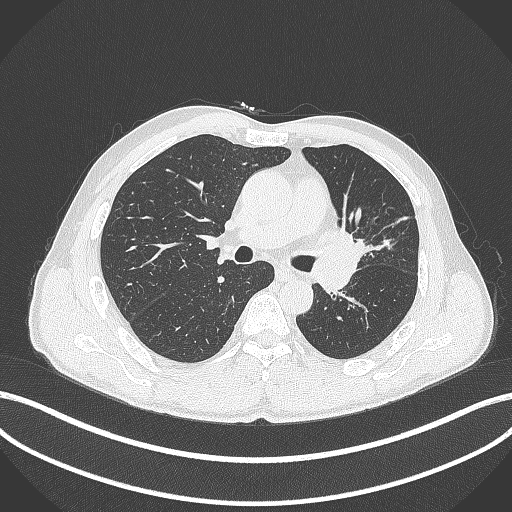
Chest CT, one axial slice; slice 251 of 429 in the series (ordered by position); reconstruction kernel B70f; 120 kVp; lung window (W 1500 / L -600 HU); 1 mm slice thickness; 512 × 512 image matrix. Male patient, age 57 years. Case-level facts recorded for this patient, not image findings: clinical TNM (as recorded): T2b N0 M0.
Outlined on this slice (bounding box drawn by a radiologist):
- lung tumour (recorded histology: squamous cell carcinoma): bounding box [x1, y1, x2, y2] px = [319, 223, 367, 264]